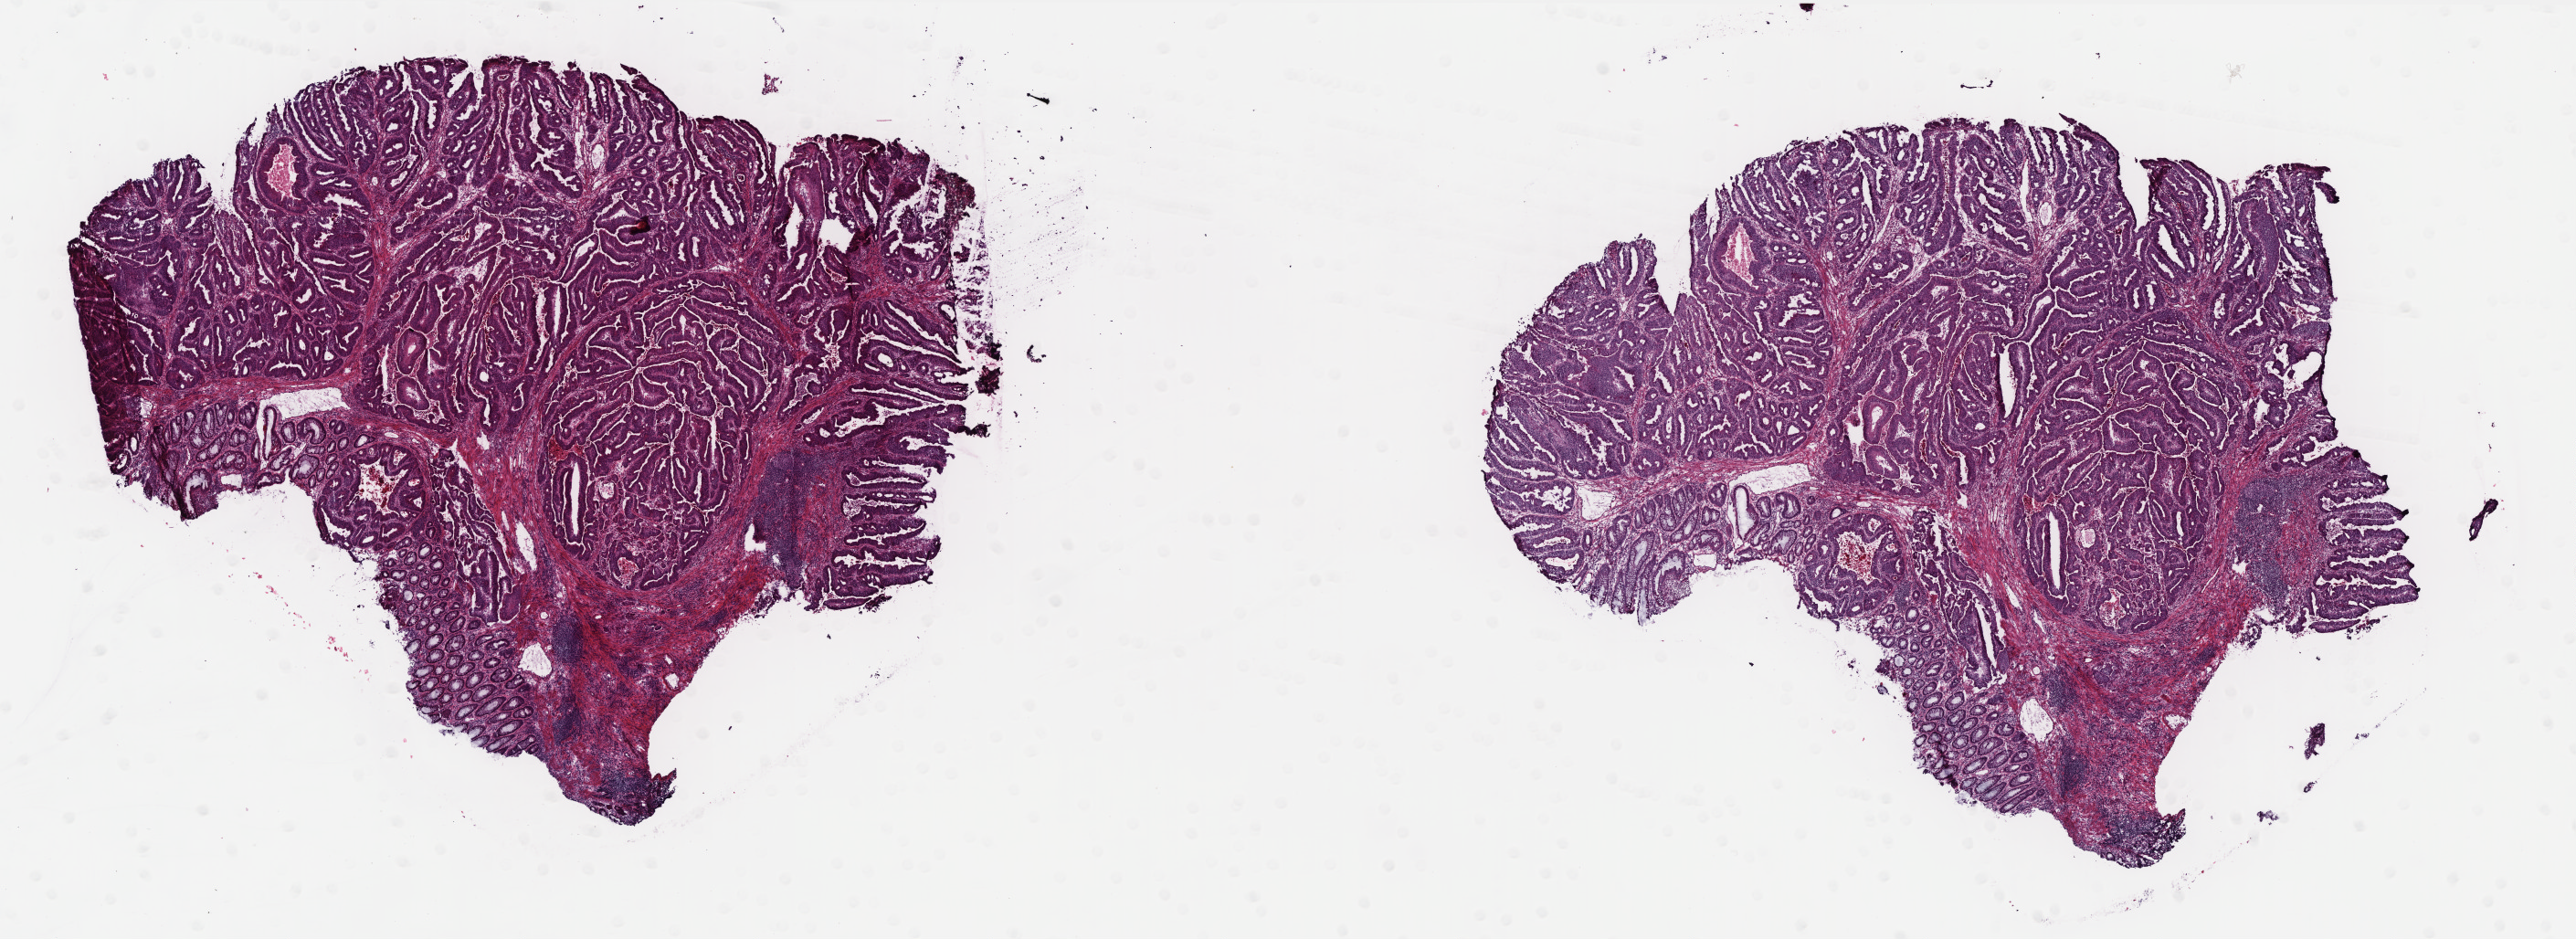
Digitized H&E tissue section (whole slide), low-resolution overview of the scanned area, about 22.6 x 8.2 mm; frozen section from the bottom of the tissue portion; primary tumour sample from the colon. Male patient; age at initial diagnosis 72 years. Composition of this section per pathologist review: tumour cells 75%, tumour nuclei 70%, normal cells 15%, stromal cells 8%, necrosis 2%. Infiltration values recorded for this section: lymphocyte infiltration 8%, monocyte infiltration 1%, neutrophil infiltration 1%.
* histologic diagnosis: Adenocarcinoma, NOS (sigmoid colon)
* AJCC pathologic stage: IIIB